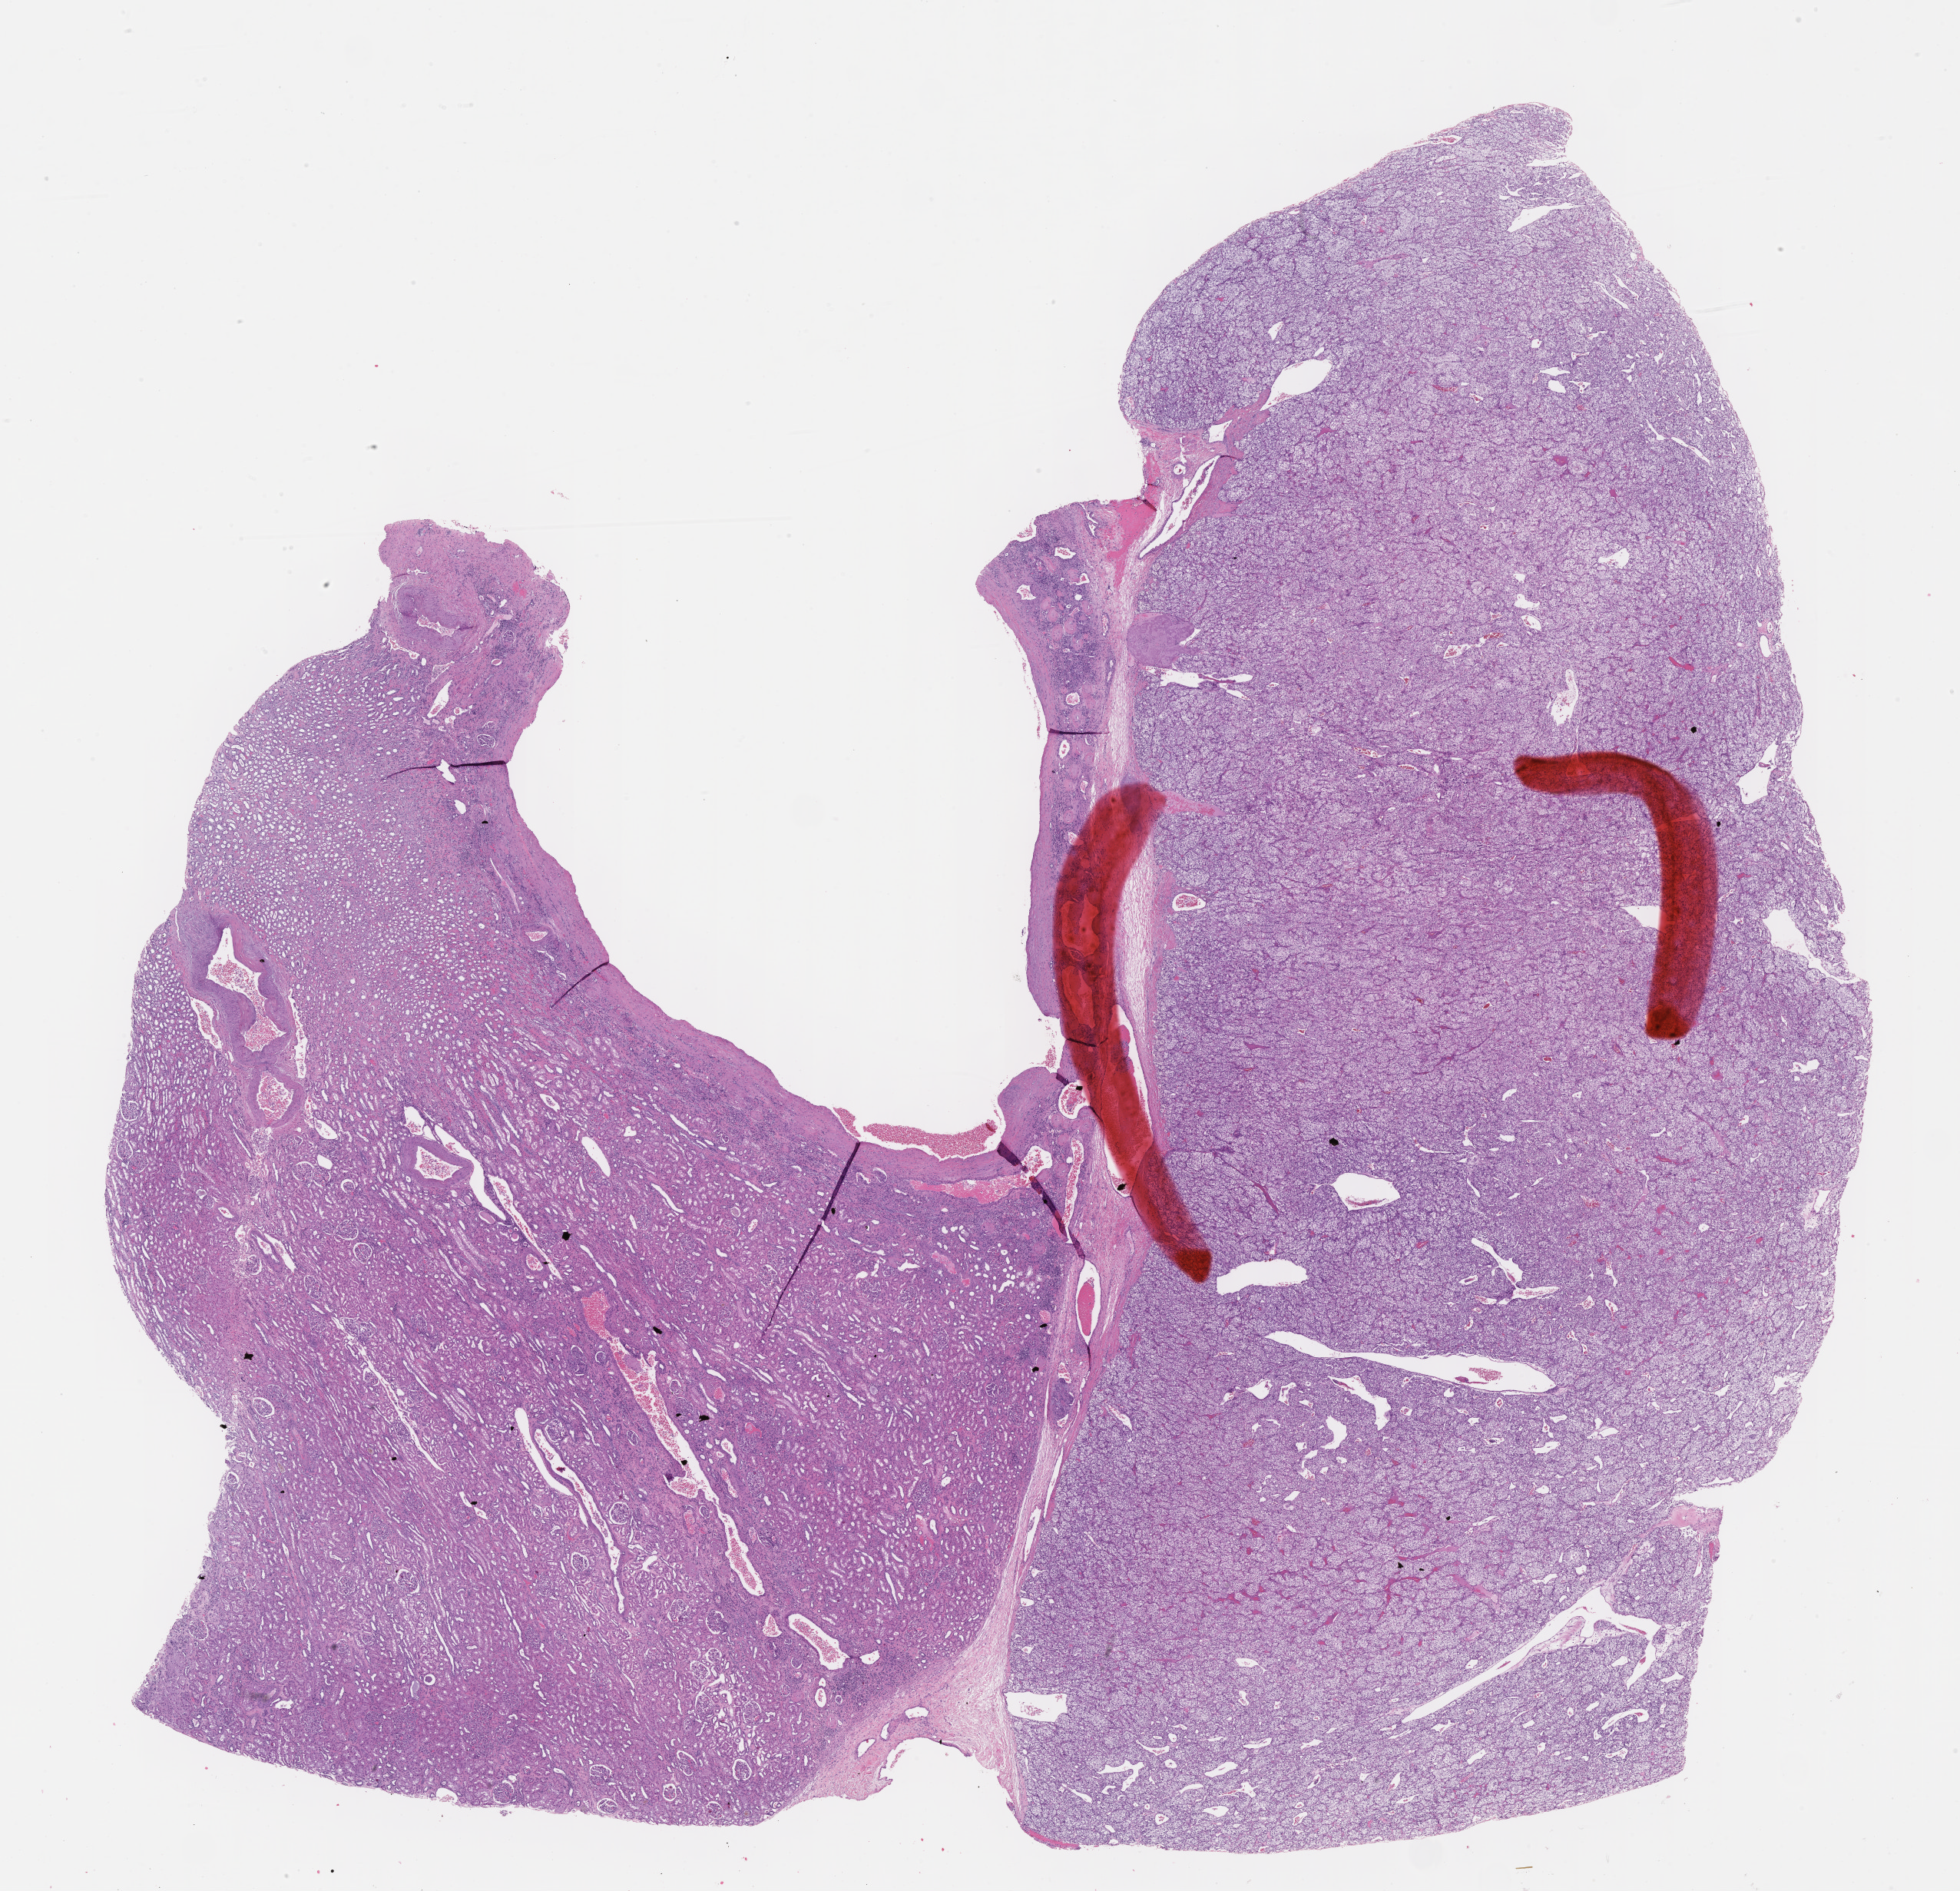
Hematoxylin and eosin (H&E) stained whole-slide image — shown as a low-resolution overview of the whole scanned area (about 20.6 x 19.9 mm, from a 40x scan), FFPE section, primary tumour sample from the kidney. Patient: male, age at initial diagnosis 61 years. Histologic grade: G3 (poorly differentiated).
• pathologic diagnosis: Clear cell adenocarcinoma, NOS
• TNM: T2 NX M0
• AJCC pathologic stage: II